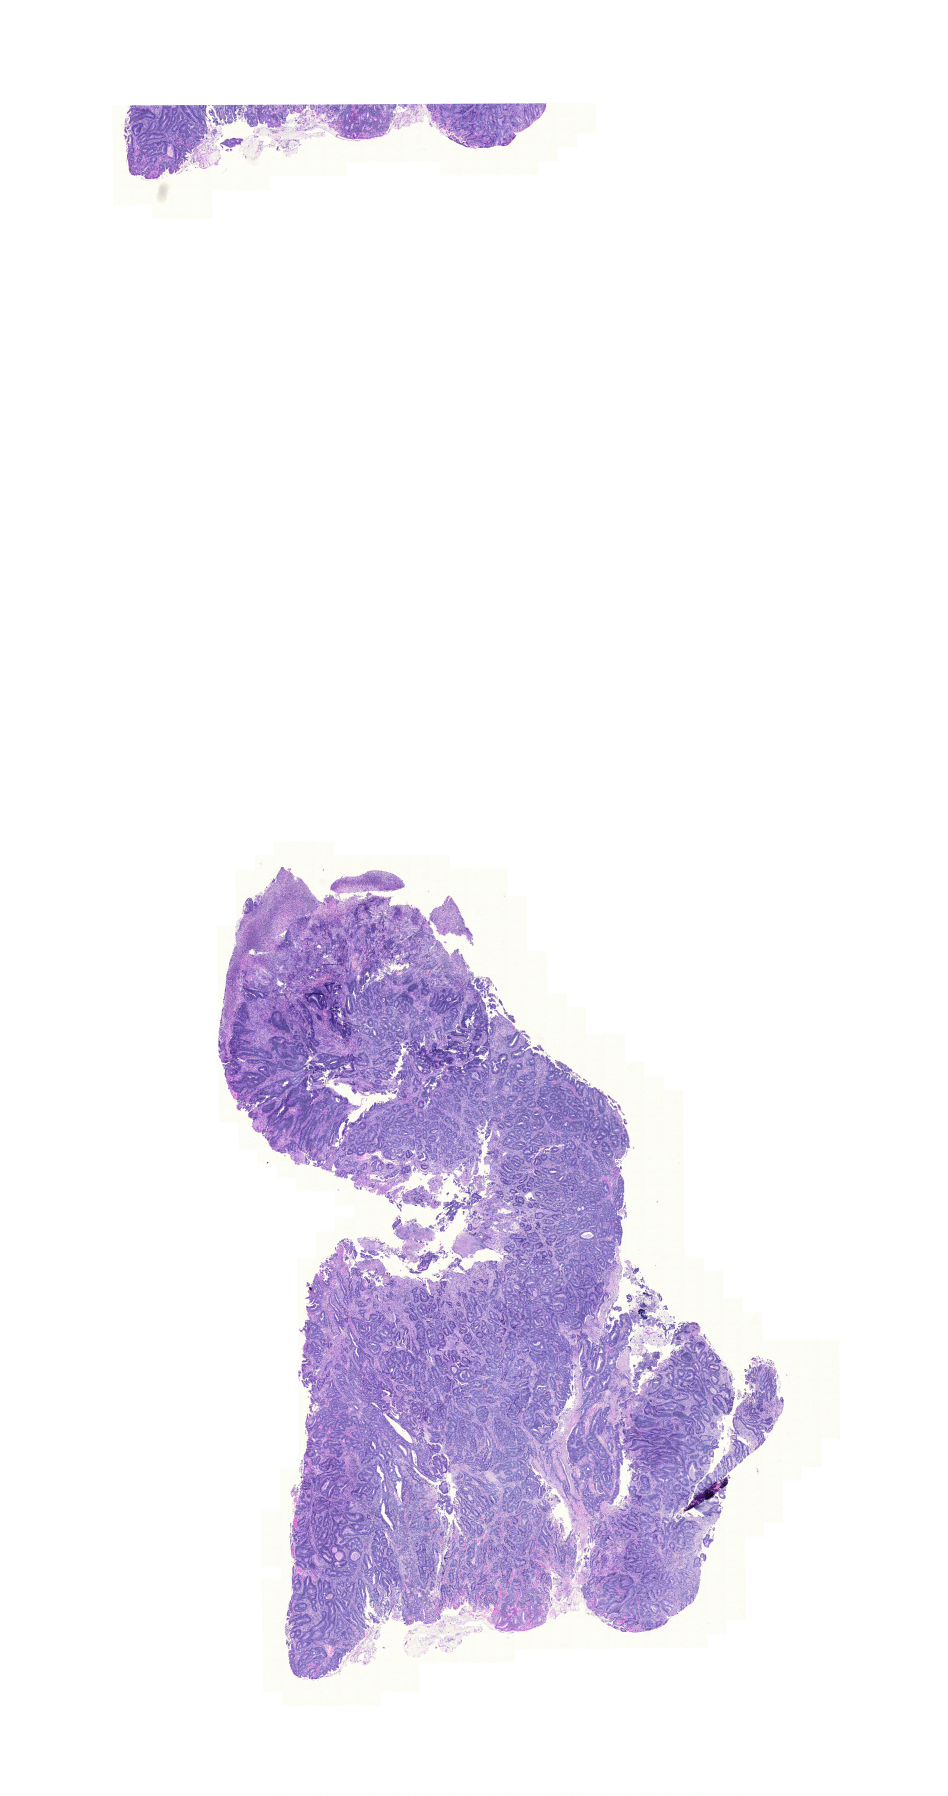
Whole-slide histology image, H&E — low-resolution overview of the scanned area, about 14.1 x 26.7 mm. FFPE section. Primary tumour sample from the colon. Male patient; age at initial diagnosis 80 years.
AJCC pathologic stage: IIA (6th edition). TNM: T3 N0 M0. Lymph nodes positive (case pathology): 0 of 34 examined. Histologic diagnosis: Adenocarcinoma, NOS (ascending colon).